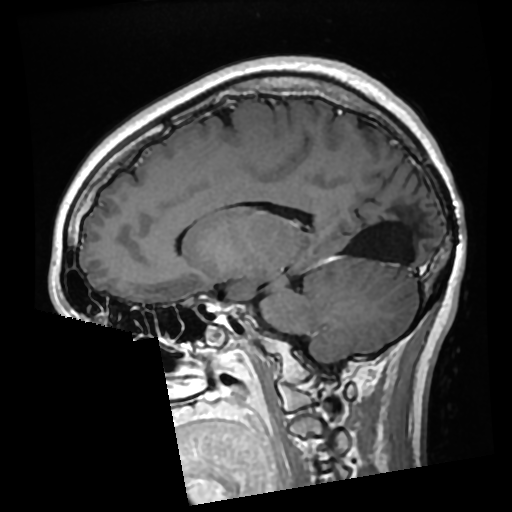
Brain MRI from a brain-tumour surgery series, one sagittal slice; slice 119 of 276 in the series (ordered by position); T1-weighted post-contrast; 0.7 mm slice thickness; 512 × 512 image matrix. From the clinical record (not read from this slice): histopathology: Glioma with ependymal features; WHO grade: 2; tumour location: Left Parietal.
Outlined on this slice (expert manual segmentation):
- previous resection cavity: bounding box (x1, y1, x2, y2) in pixels: (344, 204, 416, 262)